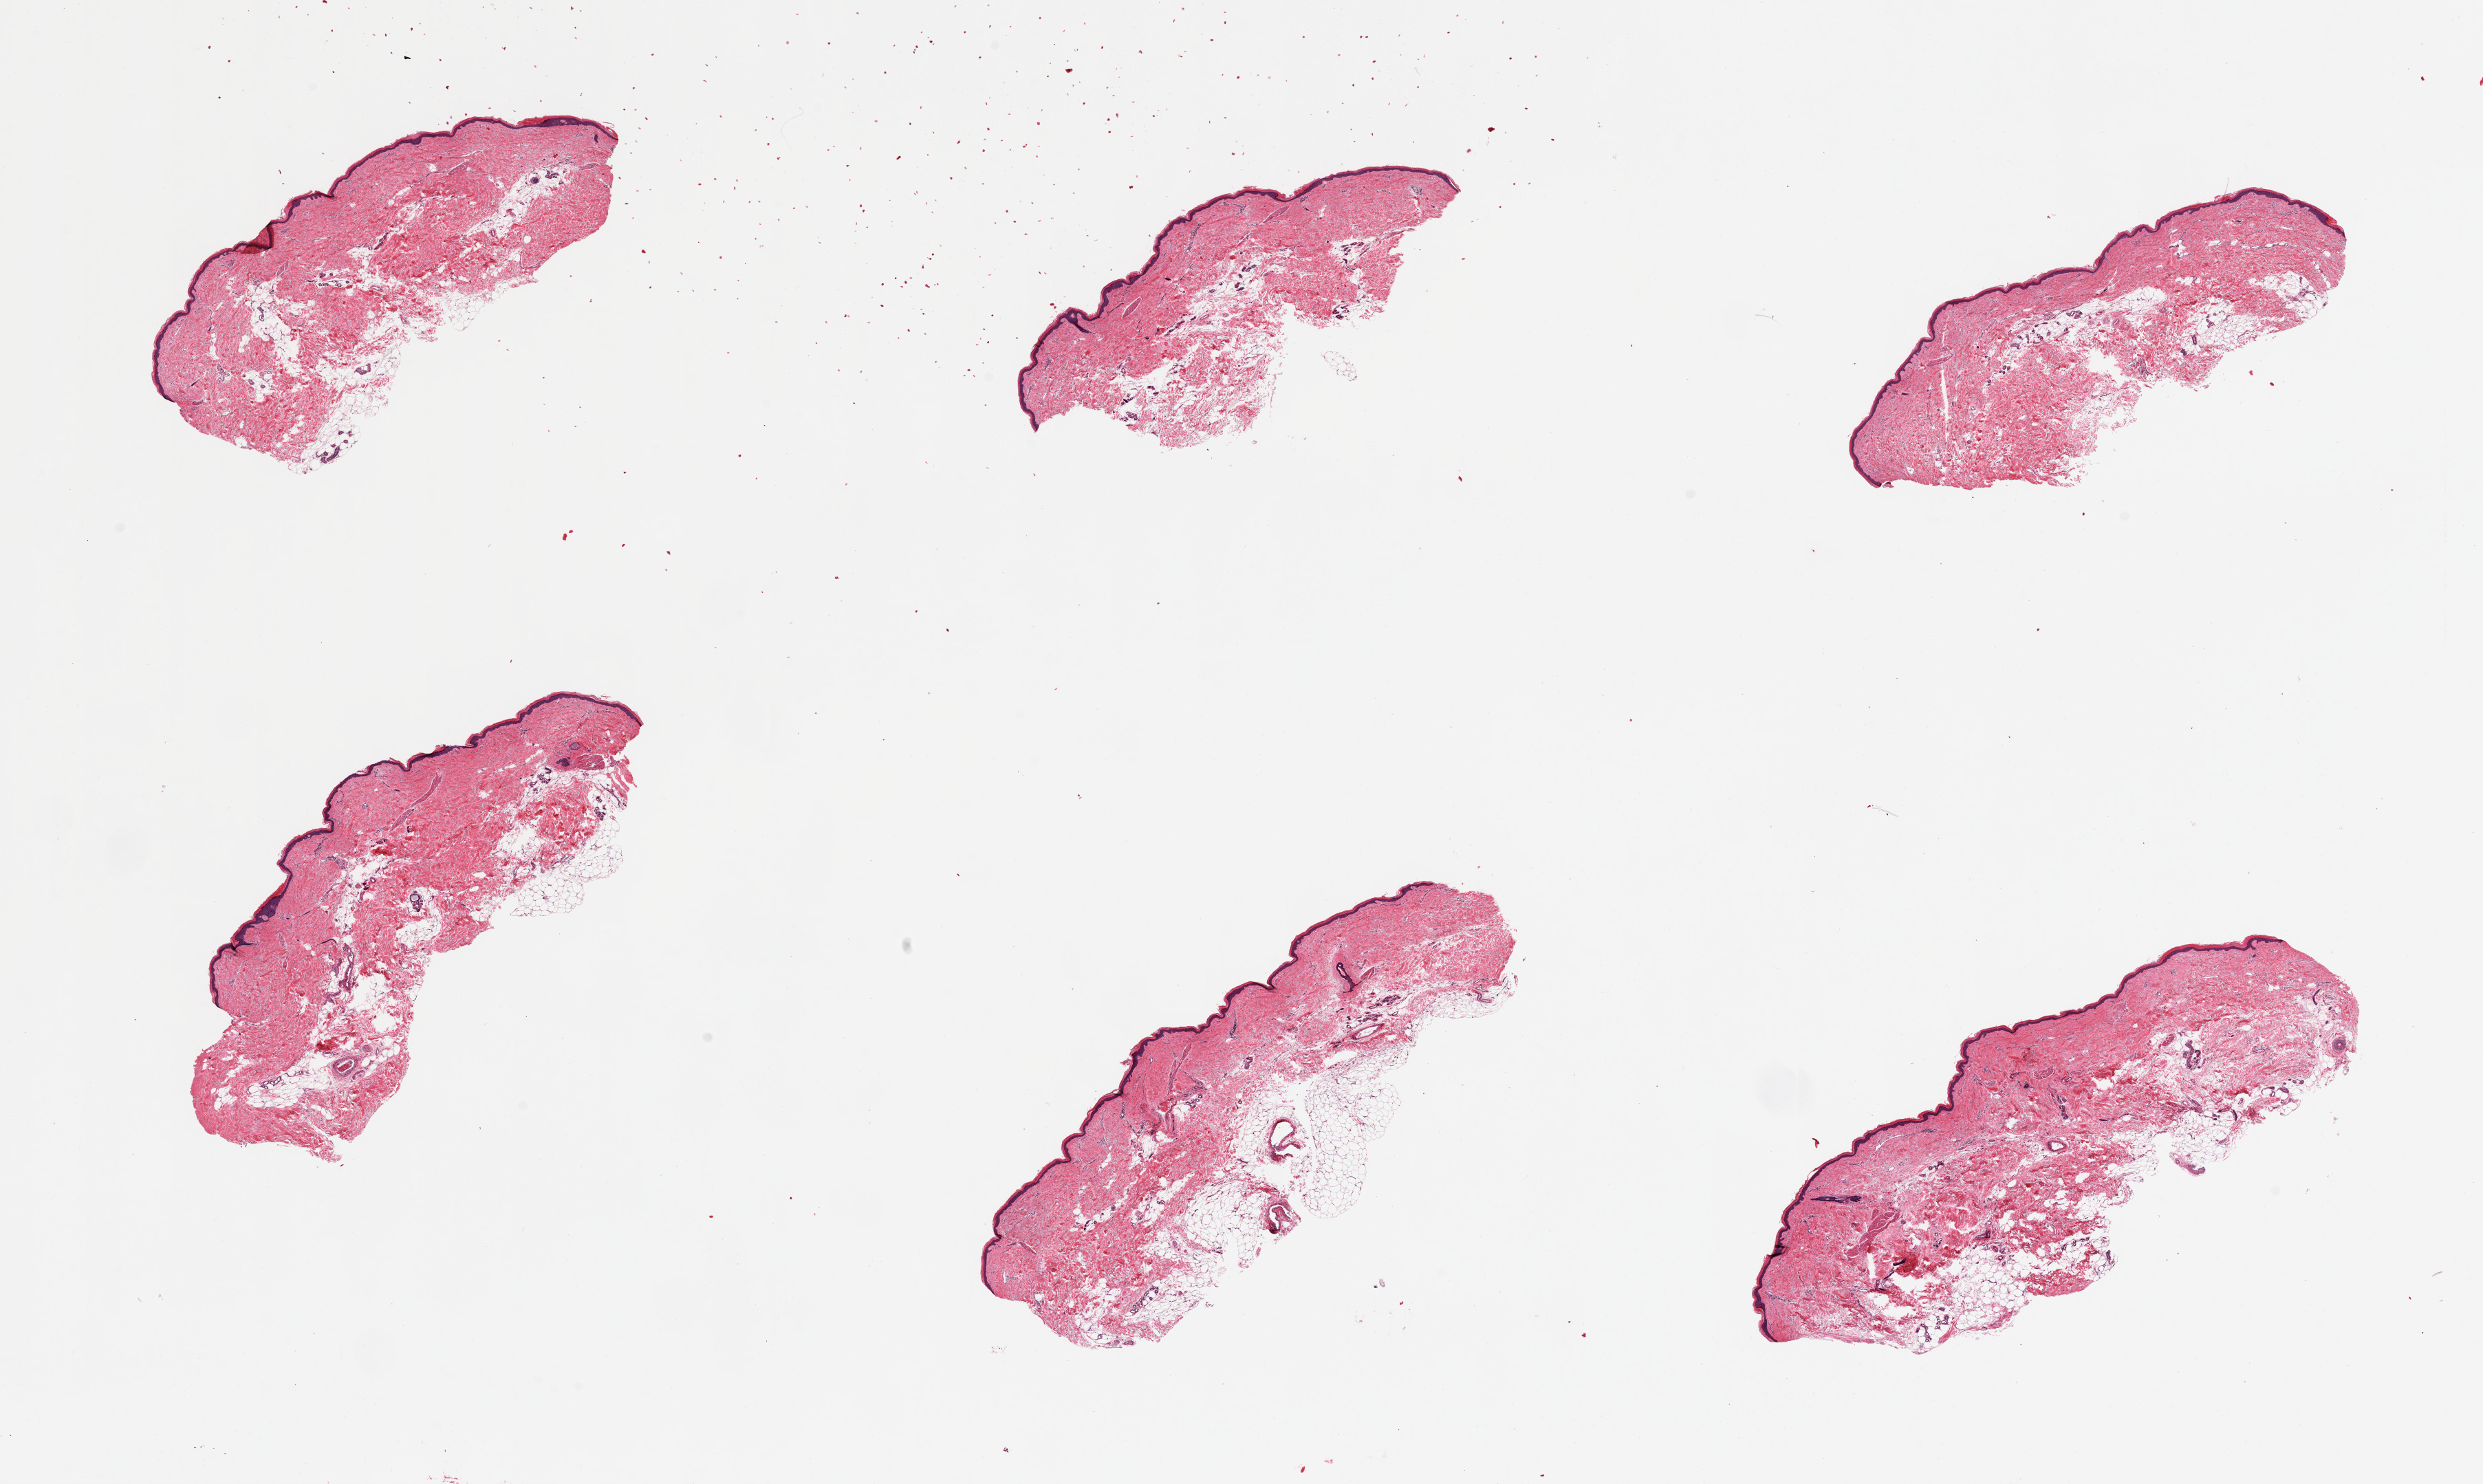
Whole-slide image, hematoxylin and eosin (H&E) stain, brightfield — a low-resolution overview of the entire scanned area, about 28.5 x 17.1 mm, PAXgene-fixed, paraffin-embedded tissue, sampled site (target tissue): skin of lower leg, donor tissue sample. Donor sex: female.
Pathologist's review note for this sample: 6 pieces, 5-30% internal and attached dermal adipose tissue. Squamous epithelium measures 35 to 60 microns thick.